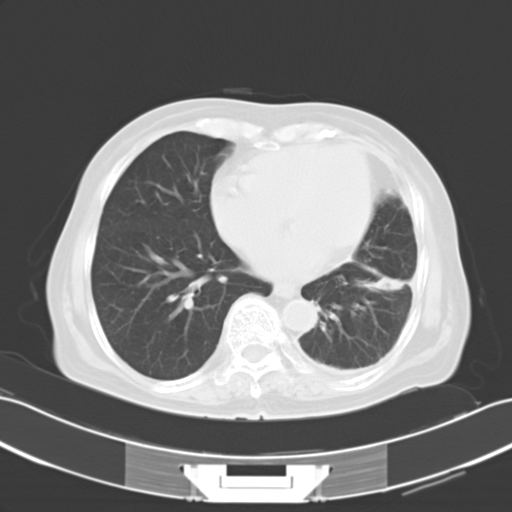
Chest CT, one axial slice; slice 12 of 29 in the series (ordered by position); lung window (W 1500 / L -600 HU); 10 mm slice thickness; 512 × 512 image matrix, field of view 353 × 353 mm. Patient: female, 82 years. Case-level facts recorded for this patient, not image findings: clinical TNM (as recorded): T1c N0 M1.
Structures marked on this image (rectangle marked by the reading radiologist):
- lung tumour (recorded histology: adenocarcinoma): bounding box [x1, y1, x2, y2] px = [363, 269, 409, 292]